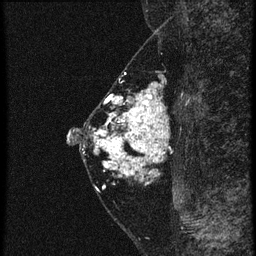
Breast MRI (dynamic contrast-enhanced), one sagittal slice. Position 26 of 60 along the scan axis. 4 images stored at this slice position (order not interpretable as contrast timing). 1.5 T. TE 4.2 ms, TR 20.4 ms. 1.5 mm slice thickness. 256 × 256 image matrix, field of view 180 × 180 mm. Patient: female, 46 years. Case-level facts recorded for this patient, not image findings: setting: breast cancer imaged before/during neoadjuvant chemotherapy; receptor status: triple-negative.
Outlined on this slice (semi-automatic segmentation, software-assisted and operator-edited):
- analysis volume of interest (the breast-tissue region the enhancement analysis was run in; not a lesion): bounding box <88,82,169,185> (left, top, right, bottom; pixels)
- tumour enhancement mask (voxels above the 90 % enhancement threshold inside the analysis volume of interest): <94,84,169,177>